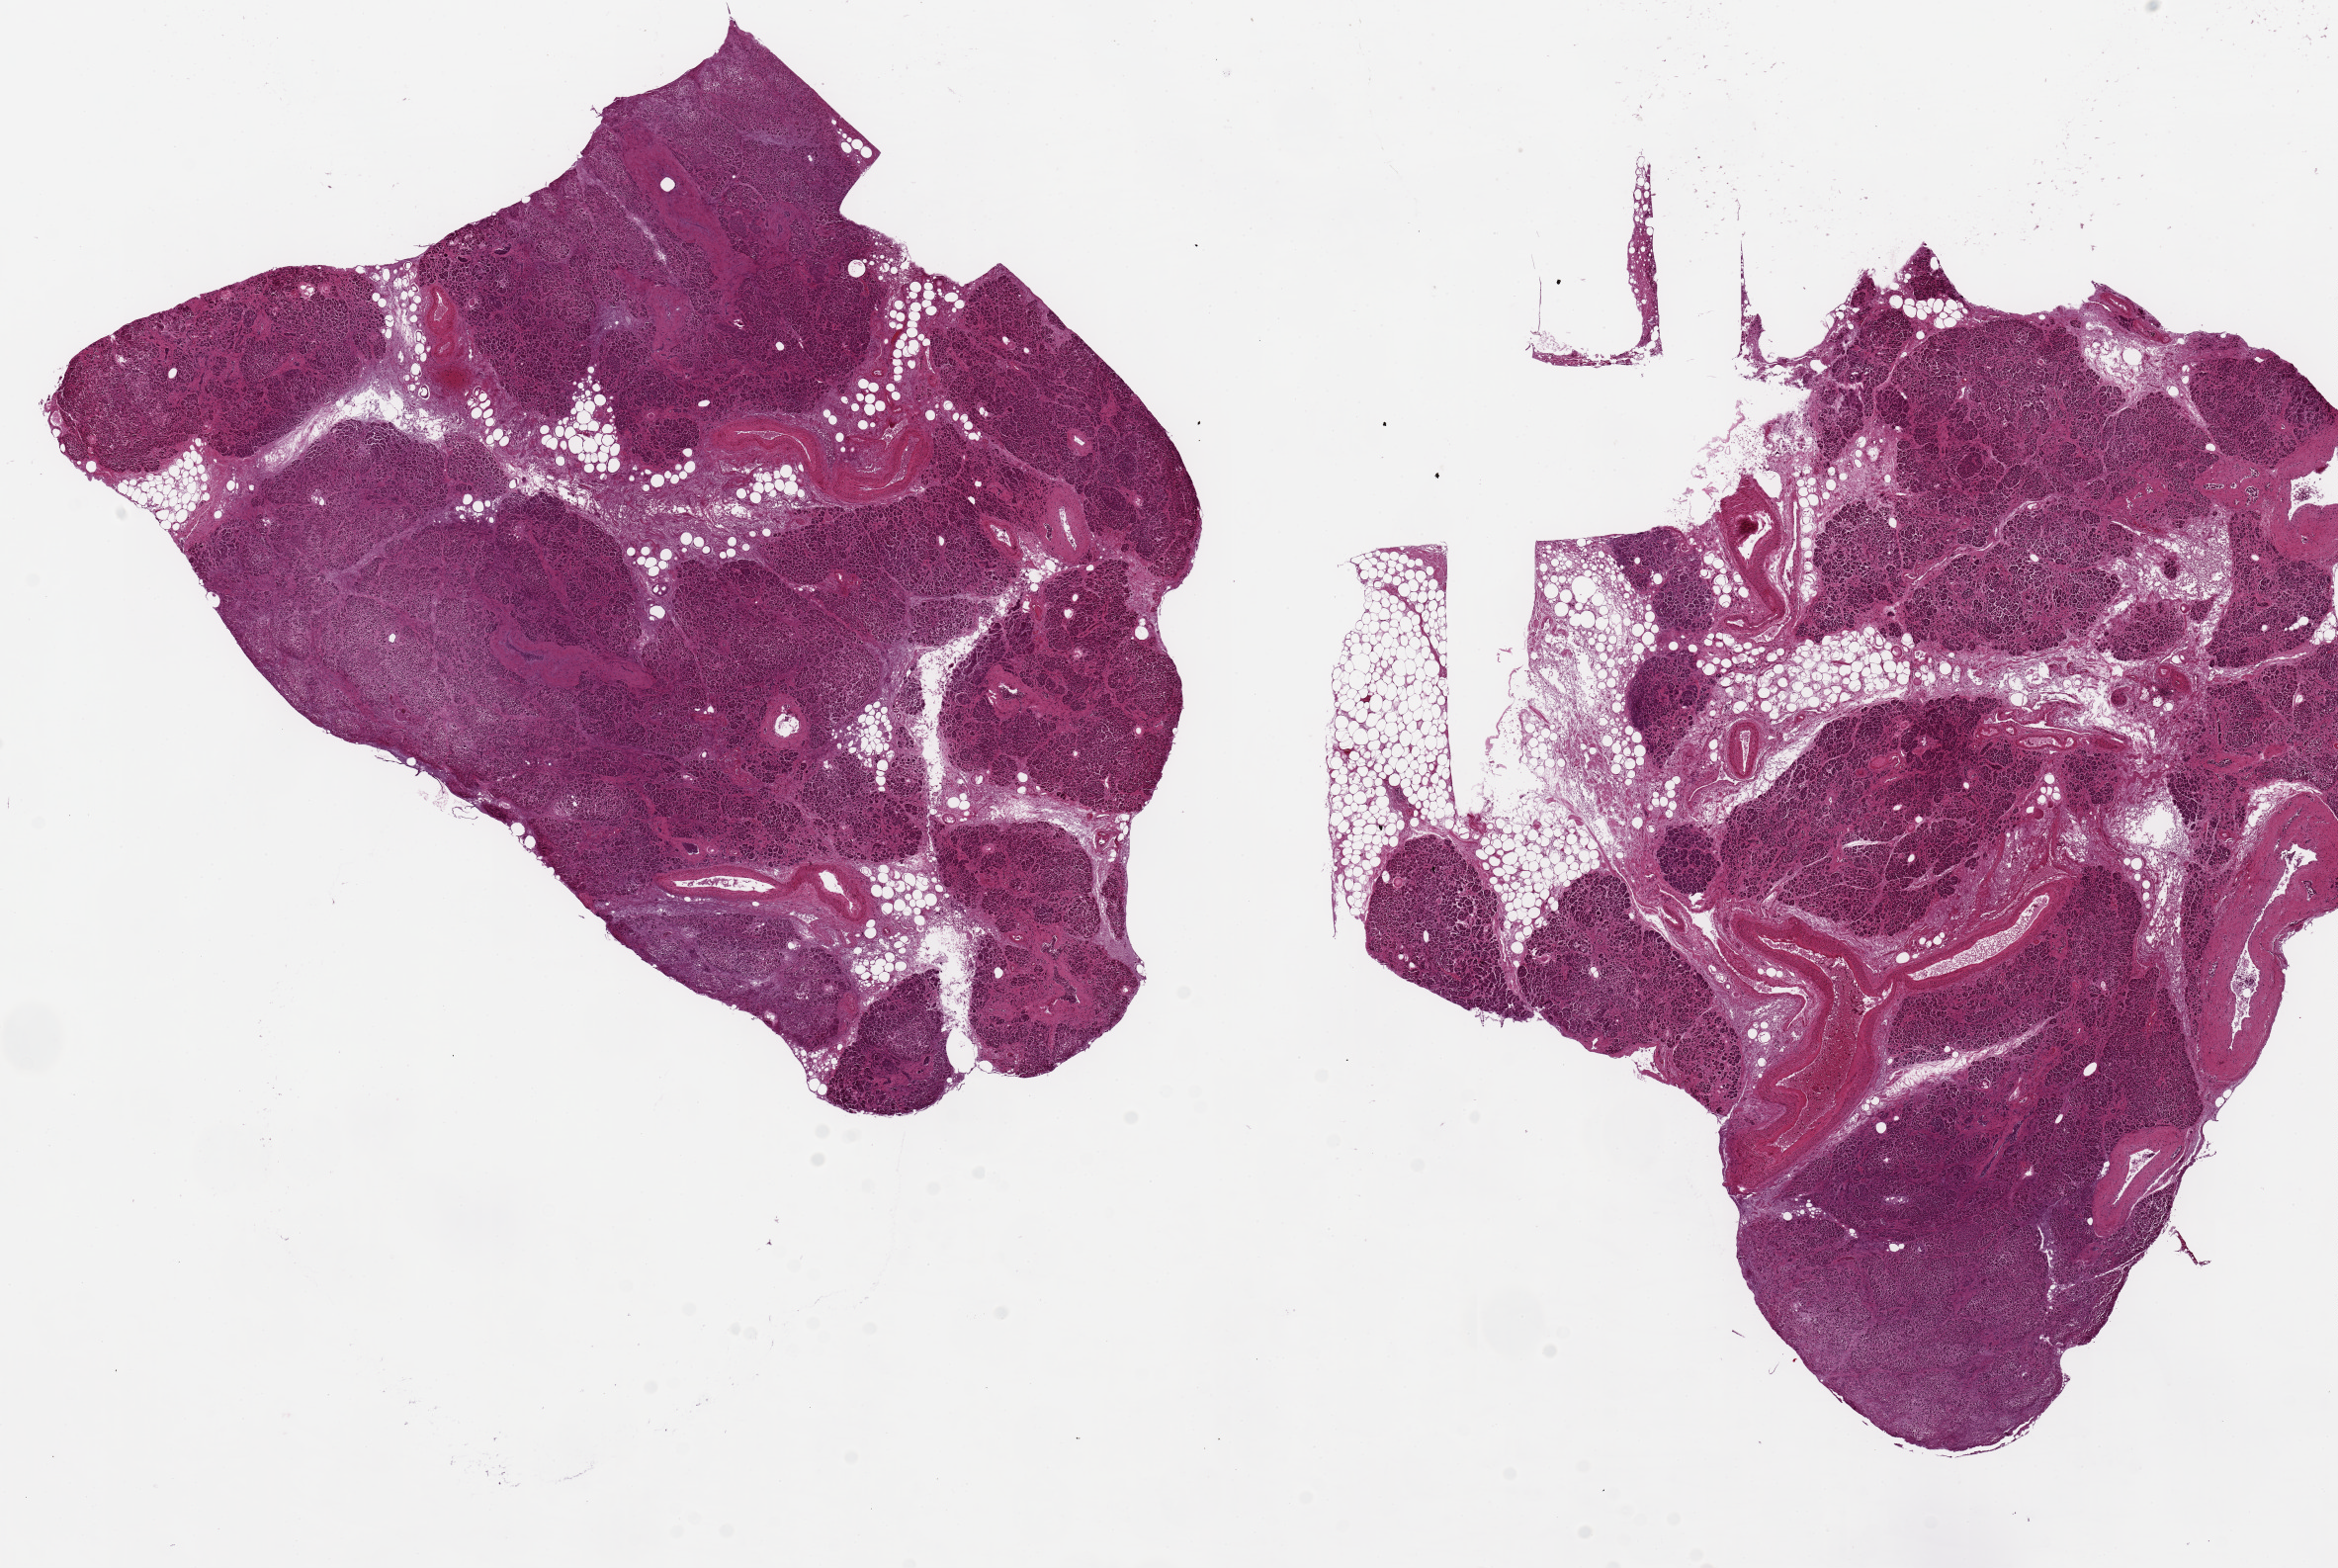
Hematoxylin and eosin (H&E) whole-slide image — shown as a low-resolution overview of the whole scanned area (about 18.7 x 12.5 mm); PAXgene-fixed paraffin-embedded (PFPE) section; sampled site (target tissue): pancreas; donor tissue sample. Female donor.
Review note (as recorded): 2 pieces; 9.5x6.5 & 10x9mm; autolysis varies from 2 to 3; 10 and 30% intra and extrapancreatic adipose.